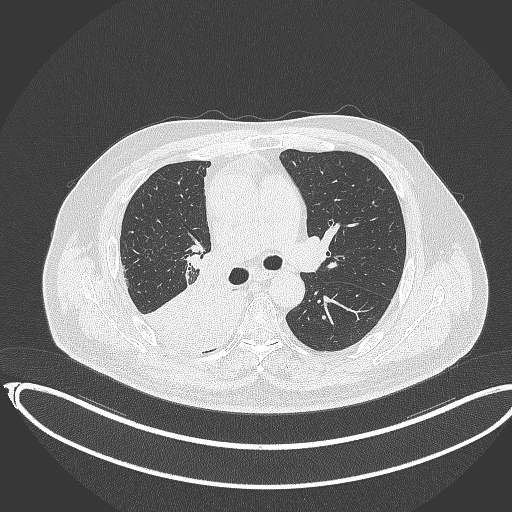
Chest CT, one axial slice. Position 217 of 403 along the scan axis. 120 kVp. Lung window (W 1500 / L -600 HU). 1 mm slice thickness. 512 × 512 image matrix, field of view 436 × 436 mm. Male patient, age 68 years. From the clinical record (not read from this slice): clinical TNM (as recorded): T2a N0 M0.
Outlined on this slice (rectangle marked by the reading radiologist):
- lung tumour (recorded histology: adenocarcinoma): bounding box (x1, y1, x2, y2) in pixels: (144, 270, 244, 351)